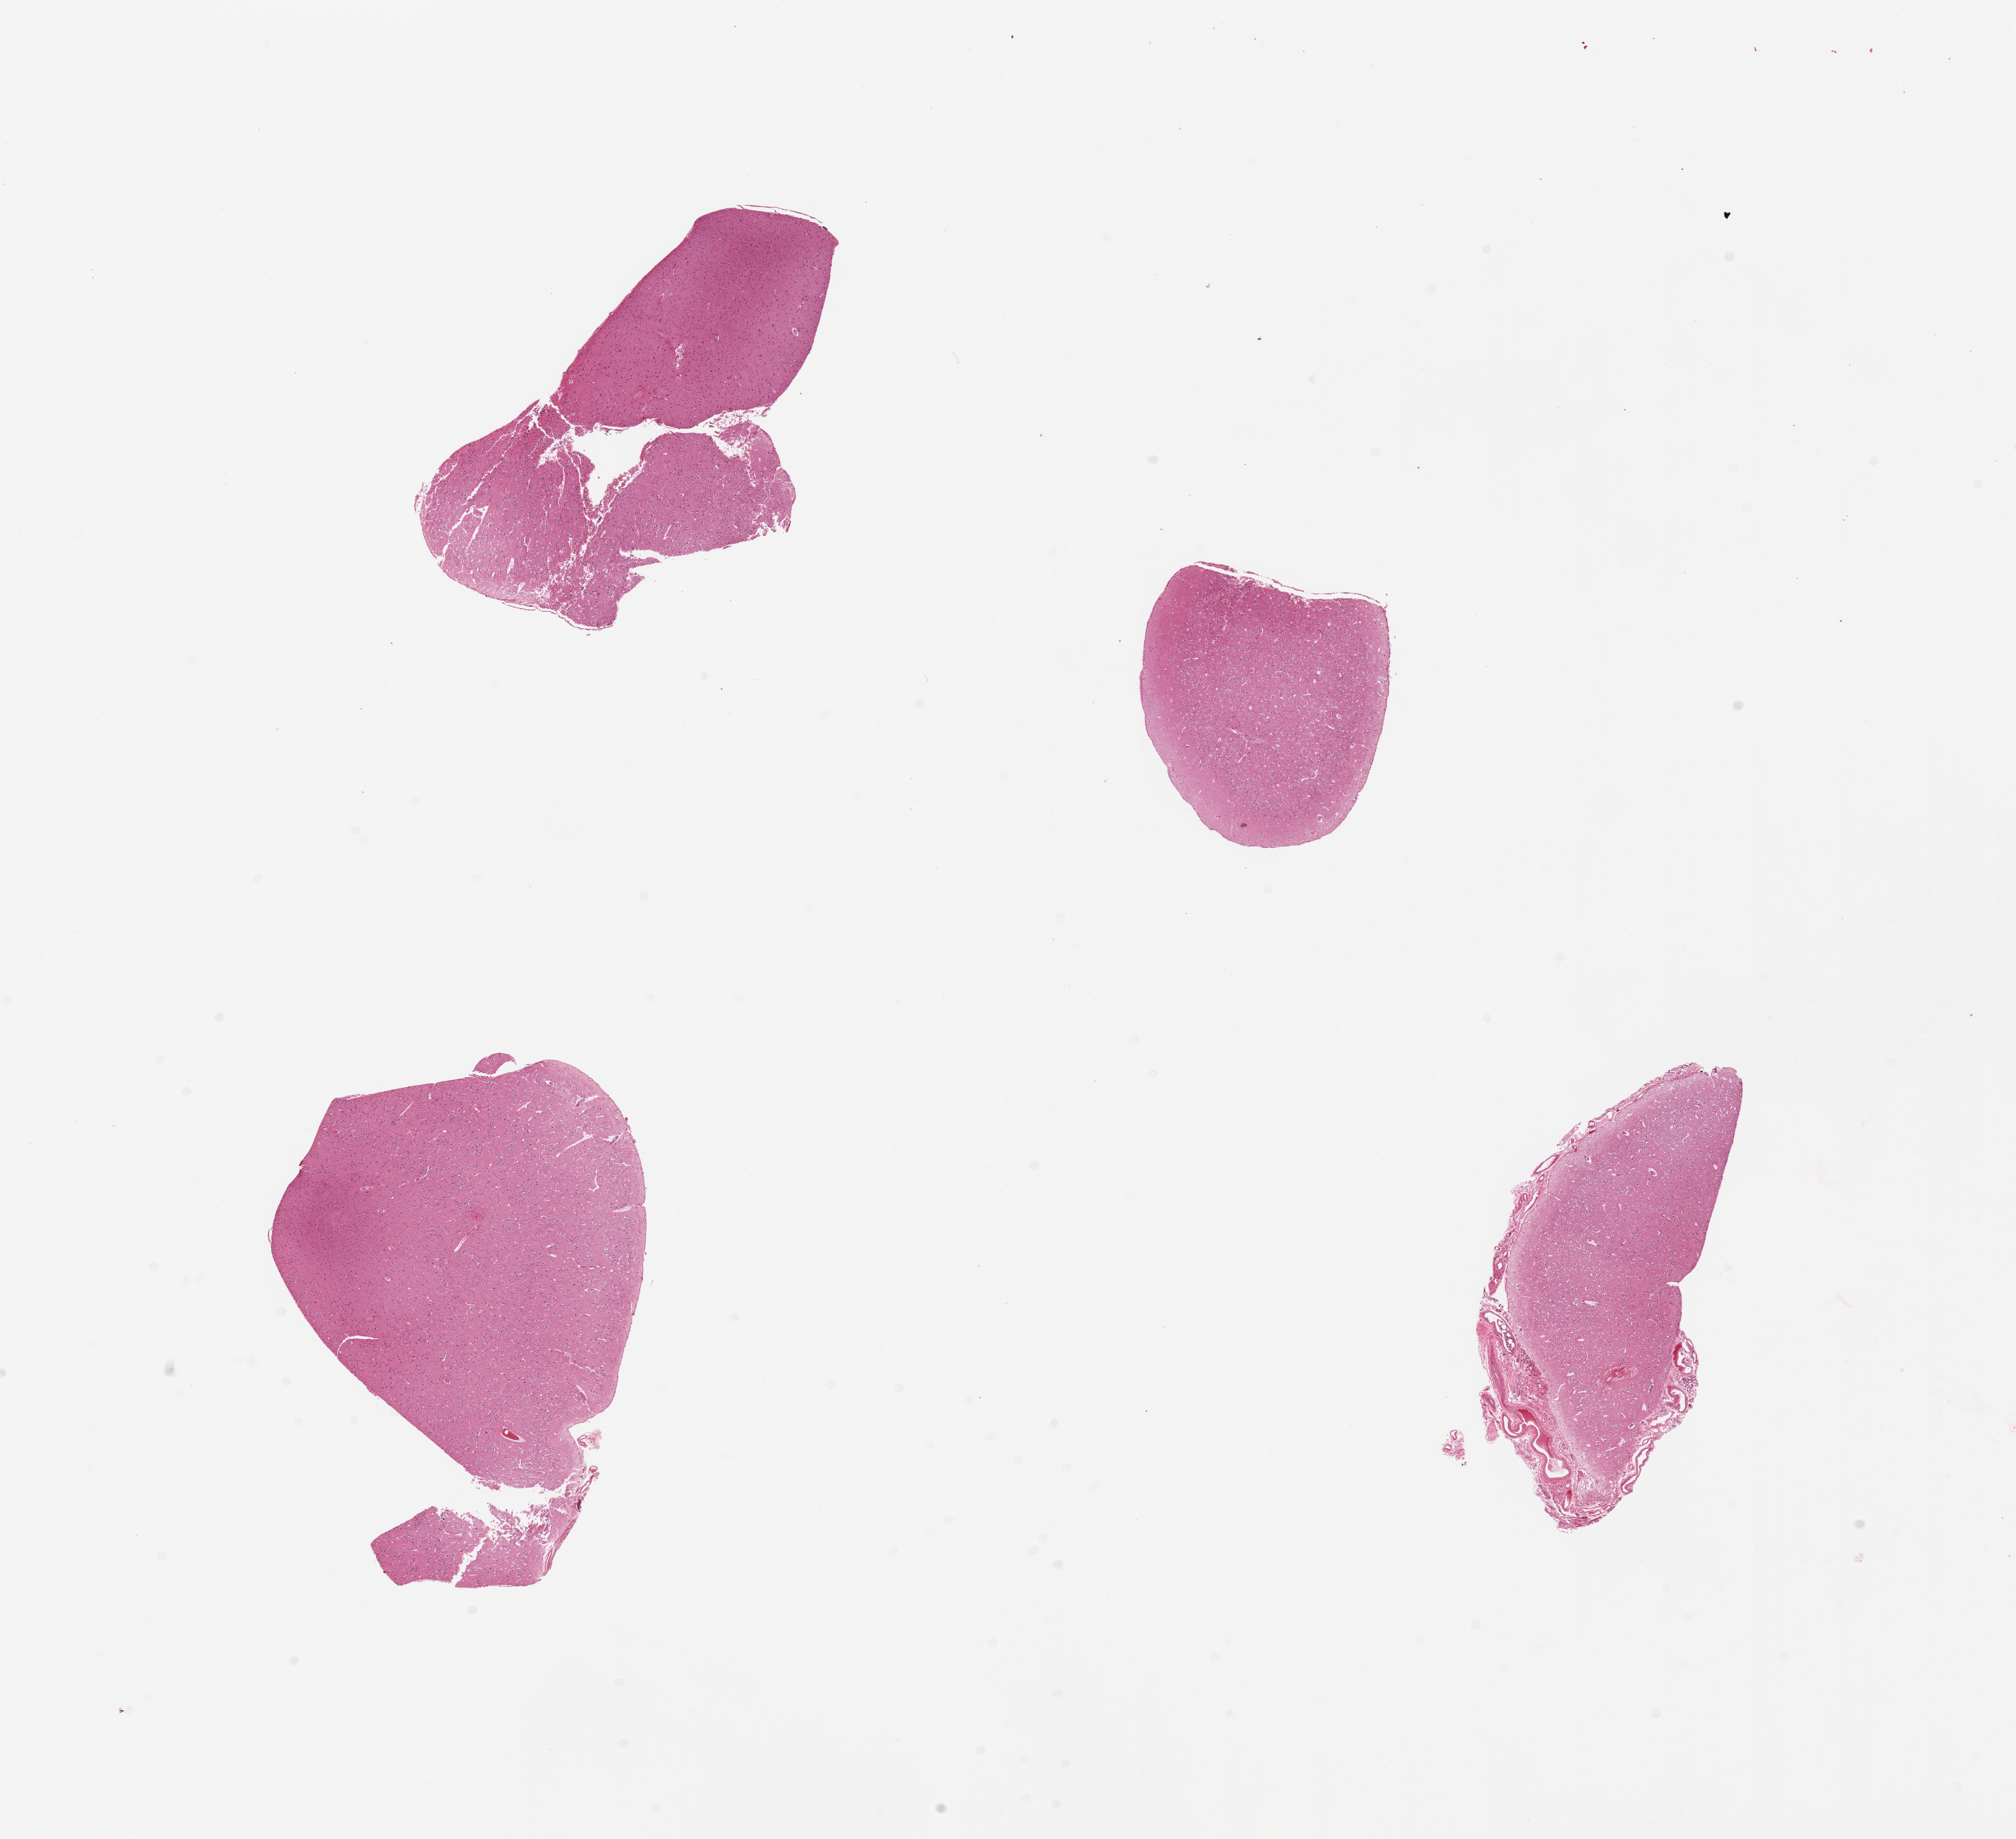
Whole-slide image, H&E stain, low-resolution overview of the scanned area, about 22.6 x 20.7 mm, PAXgene-fixed paraffin-embedded (PFPE) section, section of cerebral cortex (target tissue), donor tissue sample. Male donor.
Reviewer comment on this tissue sample: 4 pieces. Up to 0.5 mm meninges on one.